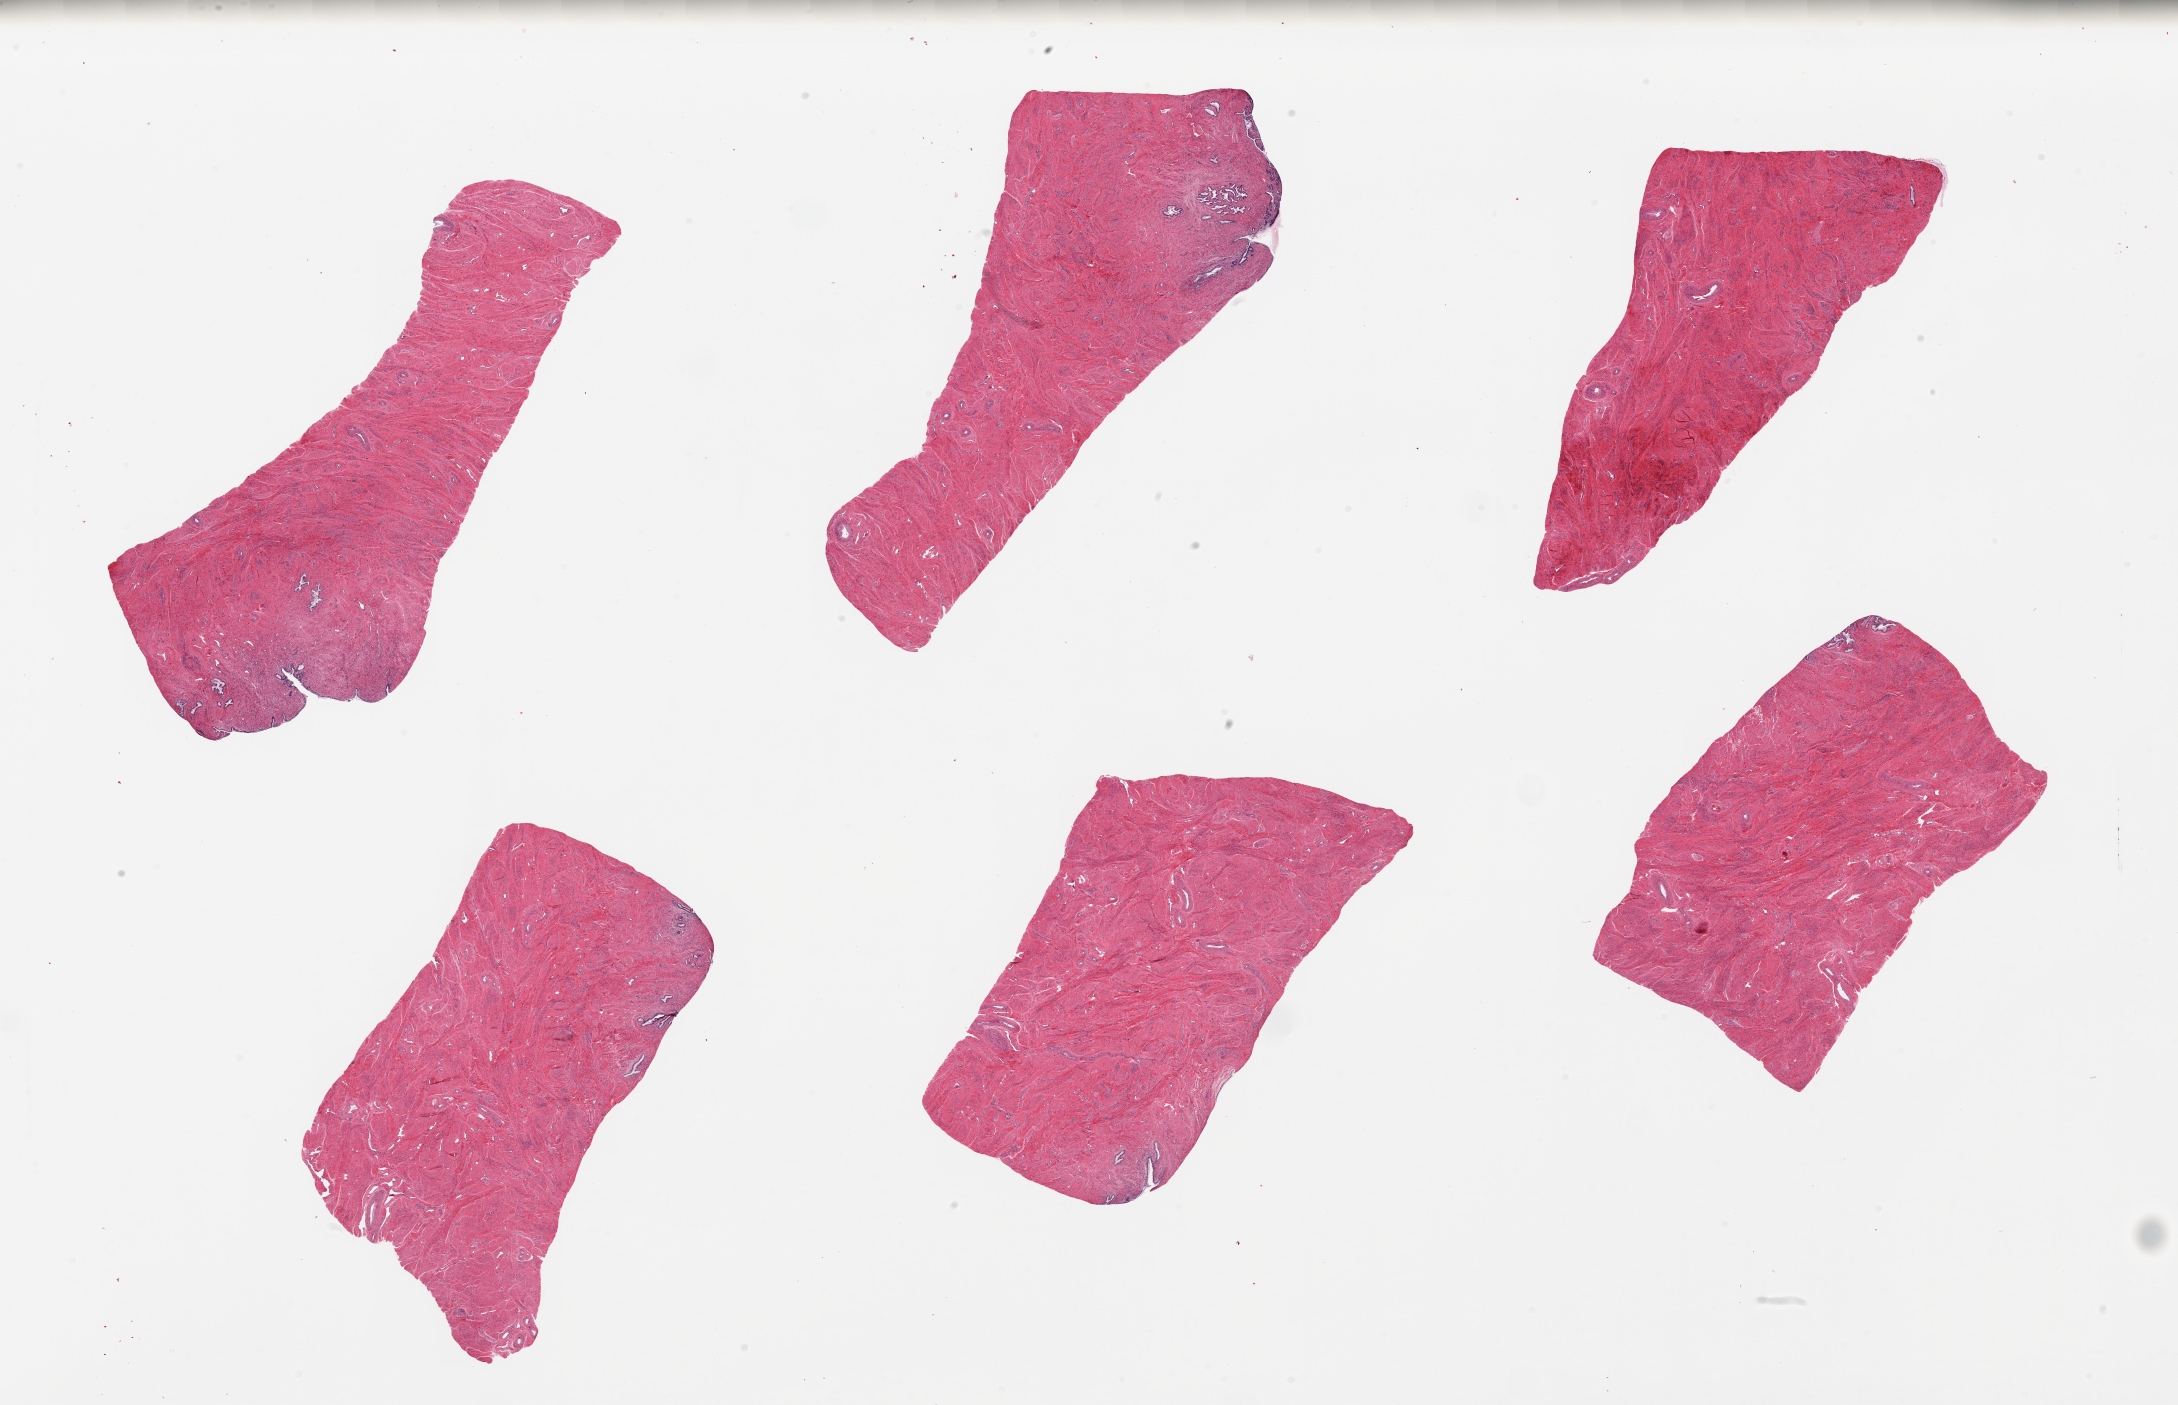
Whole-slide image, haematoxylin and eosin stain, brightfield — shown as a low-resolution overview of the whole scanned area (about 34.5 x 22.2 mm). Female donor.
Specimen: PAXgene-fixed paraffin-embedded (PFPE) section; target tissue: endocervix; donor tissue sample.